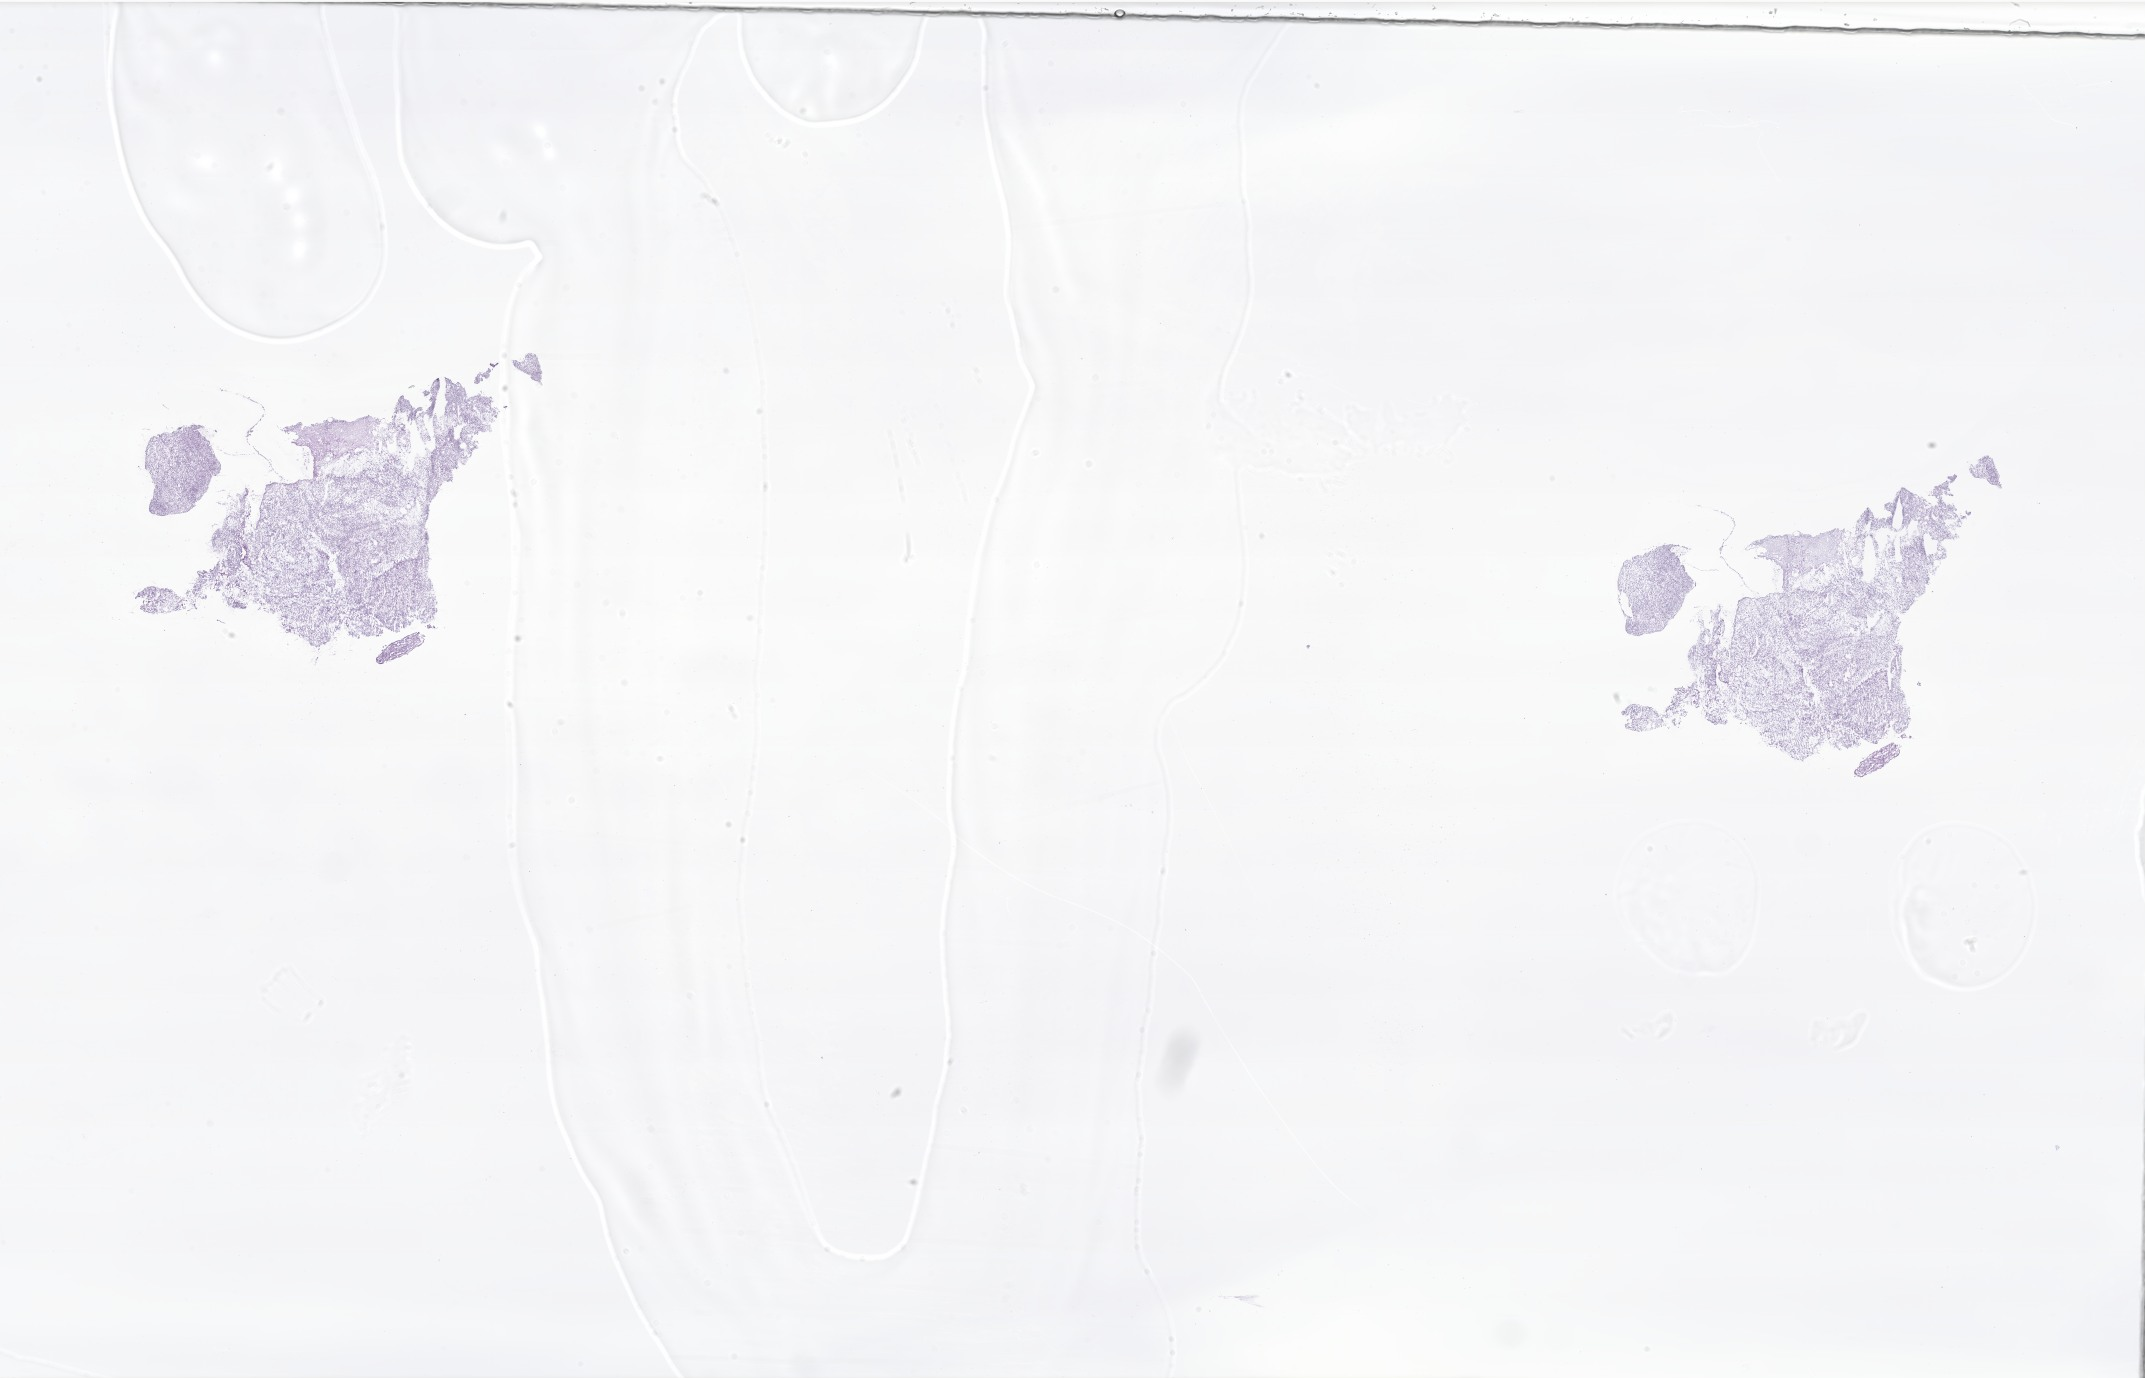
Hematoxylin and eosin (H&E) whole-slide image of tumor tissue from the cervix uteri, whole scanned area (about 36.2 x 23.2 mm) shown as a low-resolution overview, cryosection (OCT / tissue freezing medium). Patient: female, age 172 months (14 years 4 months).
- diagnosis: Embryonal rhabdomyosarcoma, NOS